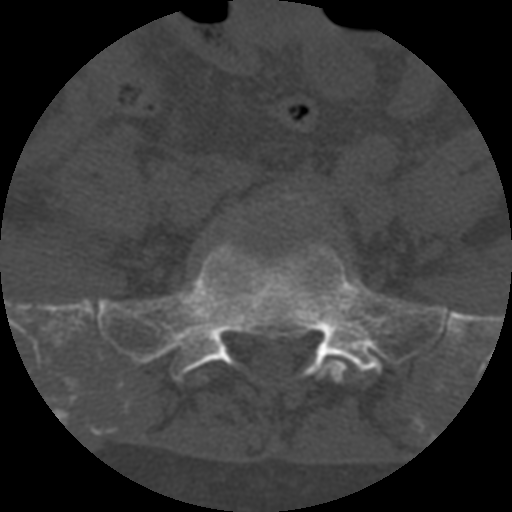
CT including the spine, one axial slice; slice 172 of 708 in the series (ordered by position); 120 kVp; one of 3 acquisitions stored at this slice position; bone window (W 1800 / L 400 HU); 512 × 512 image matrix, field of view 160 × 160 mm. Patient age 55 years. Case-level facts recorded for this patient, not image findings: primary cancer: colon.
Structures marked on this image (semi-automatically segmented with operator editing):
- L5 vertebra: bounding box [x1, y1, x2, y2] px = [196, 357, 362, 383]